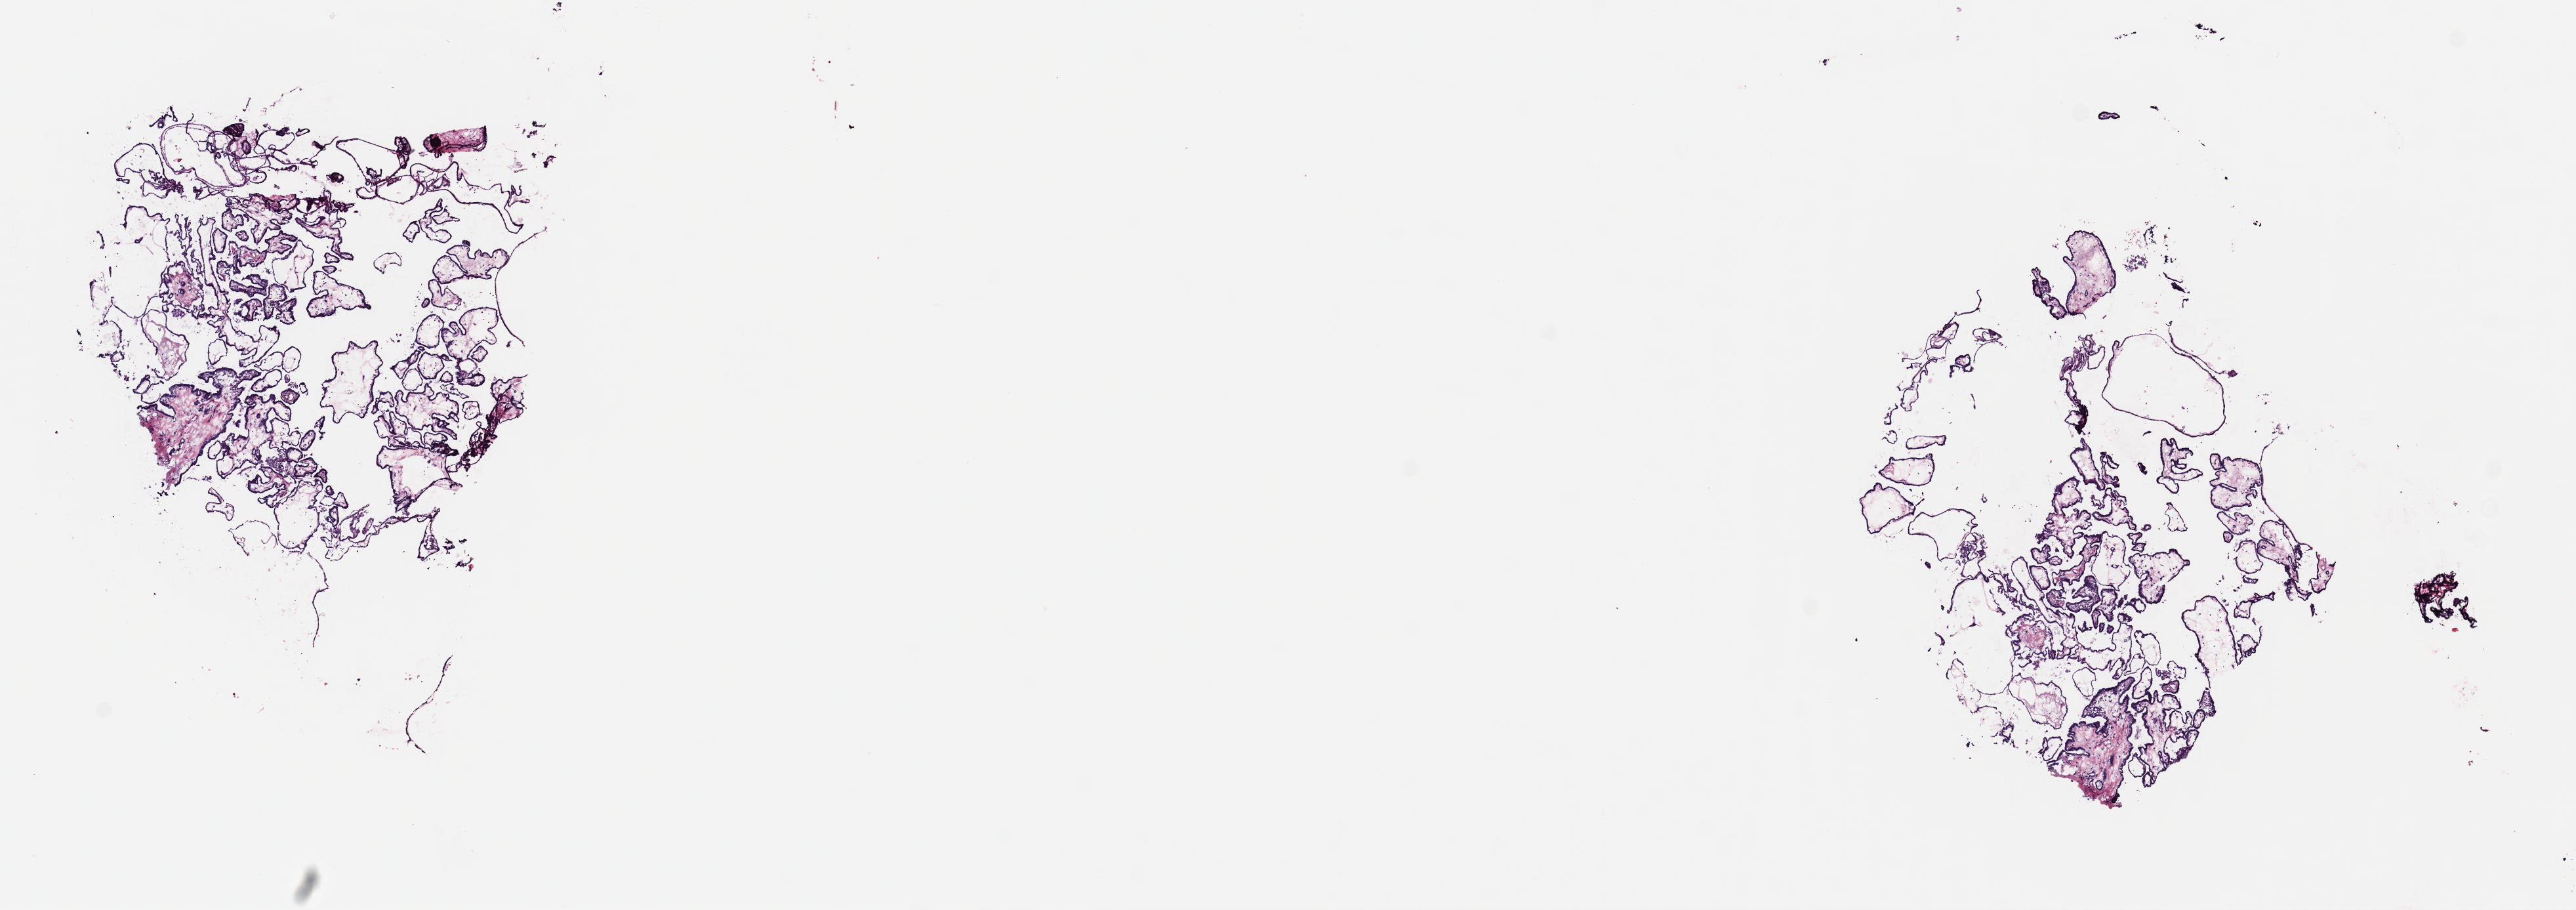
Digitized H&E tissue section (whole slide), a low-resolution overview of the entire scanned area, about 15.5 x 5.5 mm (acquisition: 40x scan); frozen section from the top of the tissue portion; sample: primary tumour, thyroid. Patient: male, age at initial diagnosis 27 years. Pathologist review of this section (percent, as recorded): tumour cells 50%, tumour nuclei 100%.
Diagnosis: Papillary adenocarcinoma, NOS (thyroid gland).